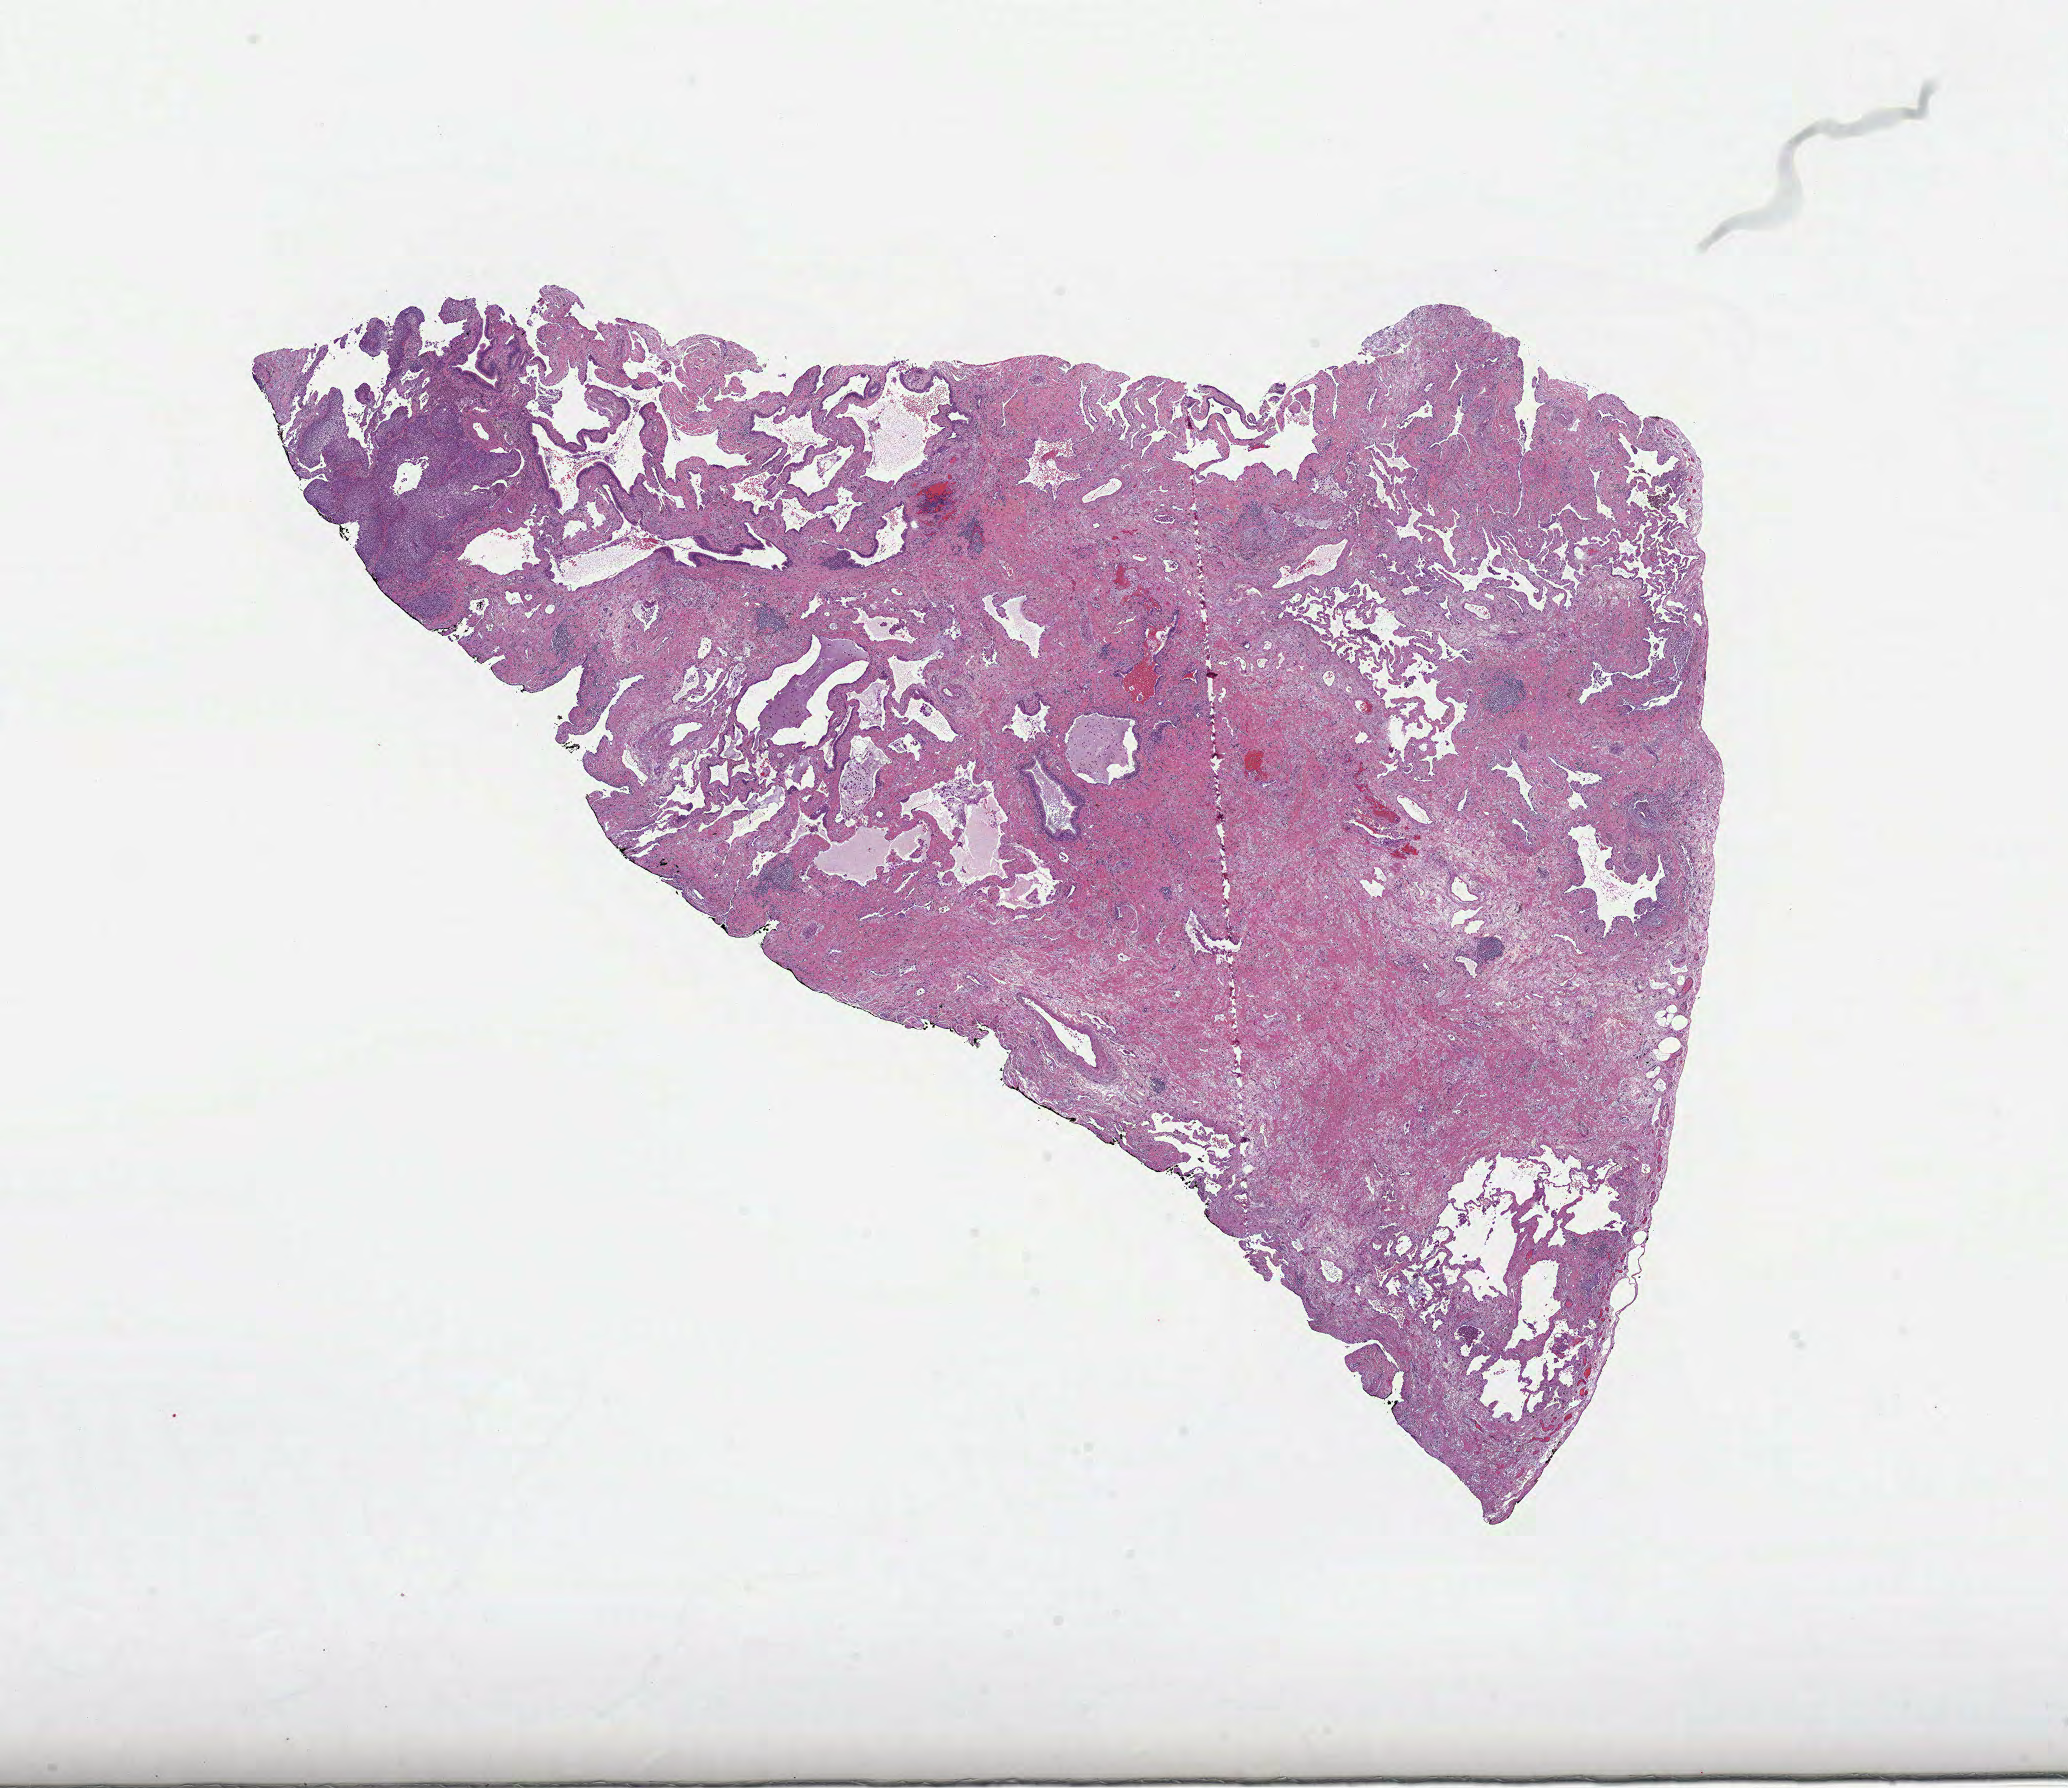
H&E whole-slide image, shown as a low-resolution overview of the whole scanned area (about 16.7 x 14.4 mm, from a 40x scan), formalin-fixed paraffin-embedded (FFPE) diagnostic section, lung, primary tumour sample. Female patient; age at initial diagnosis 72 years.
Diagnosis: Squamous cell carcinoma, NOS. AJCC pathologic stage: IB (7th edition).